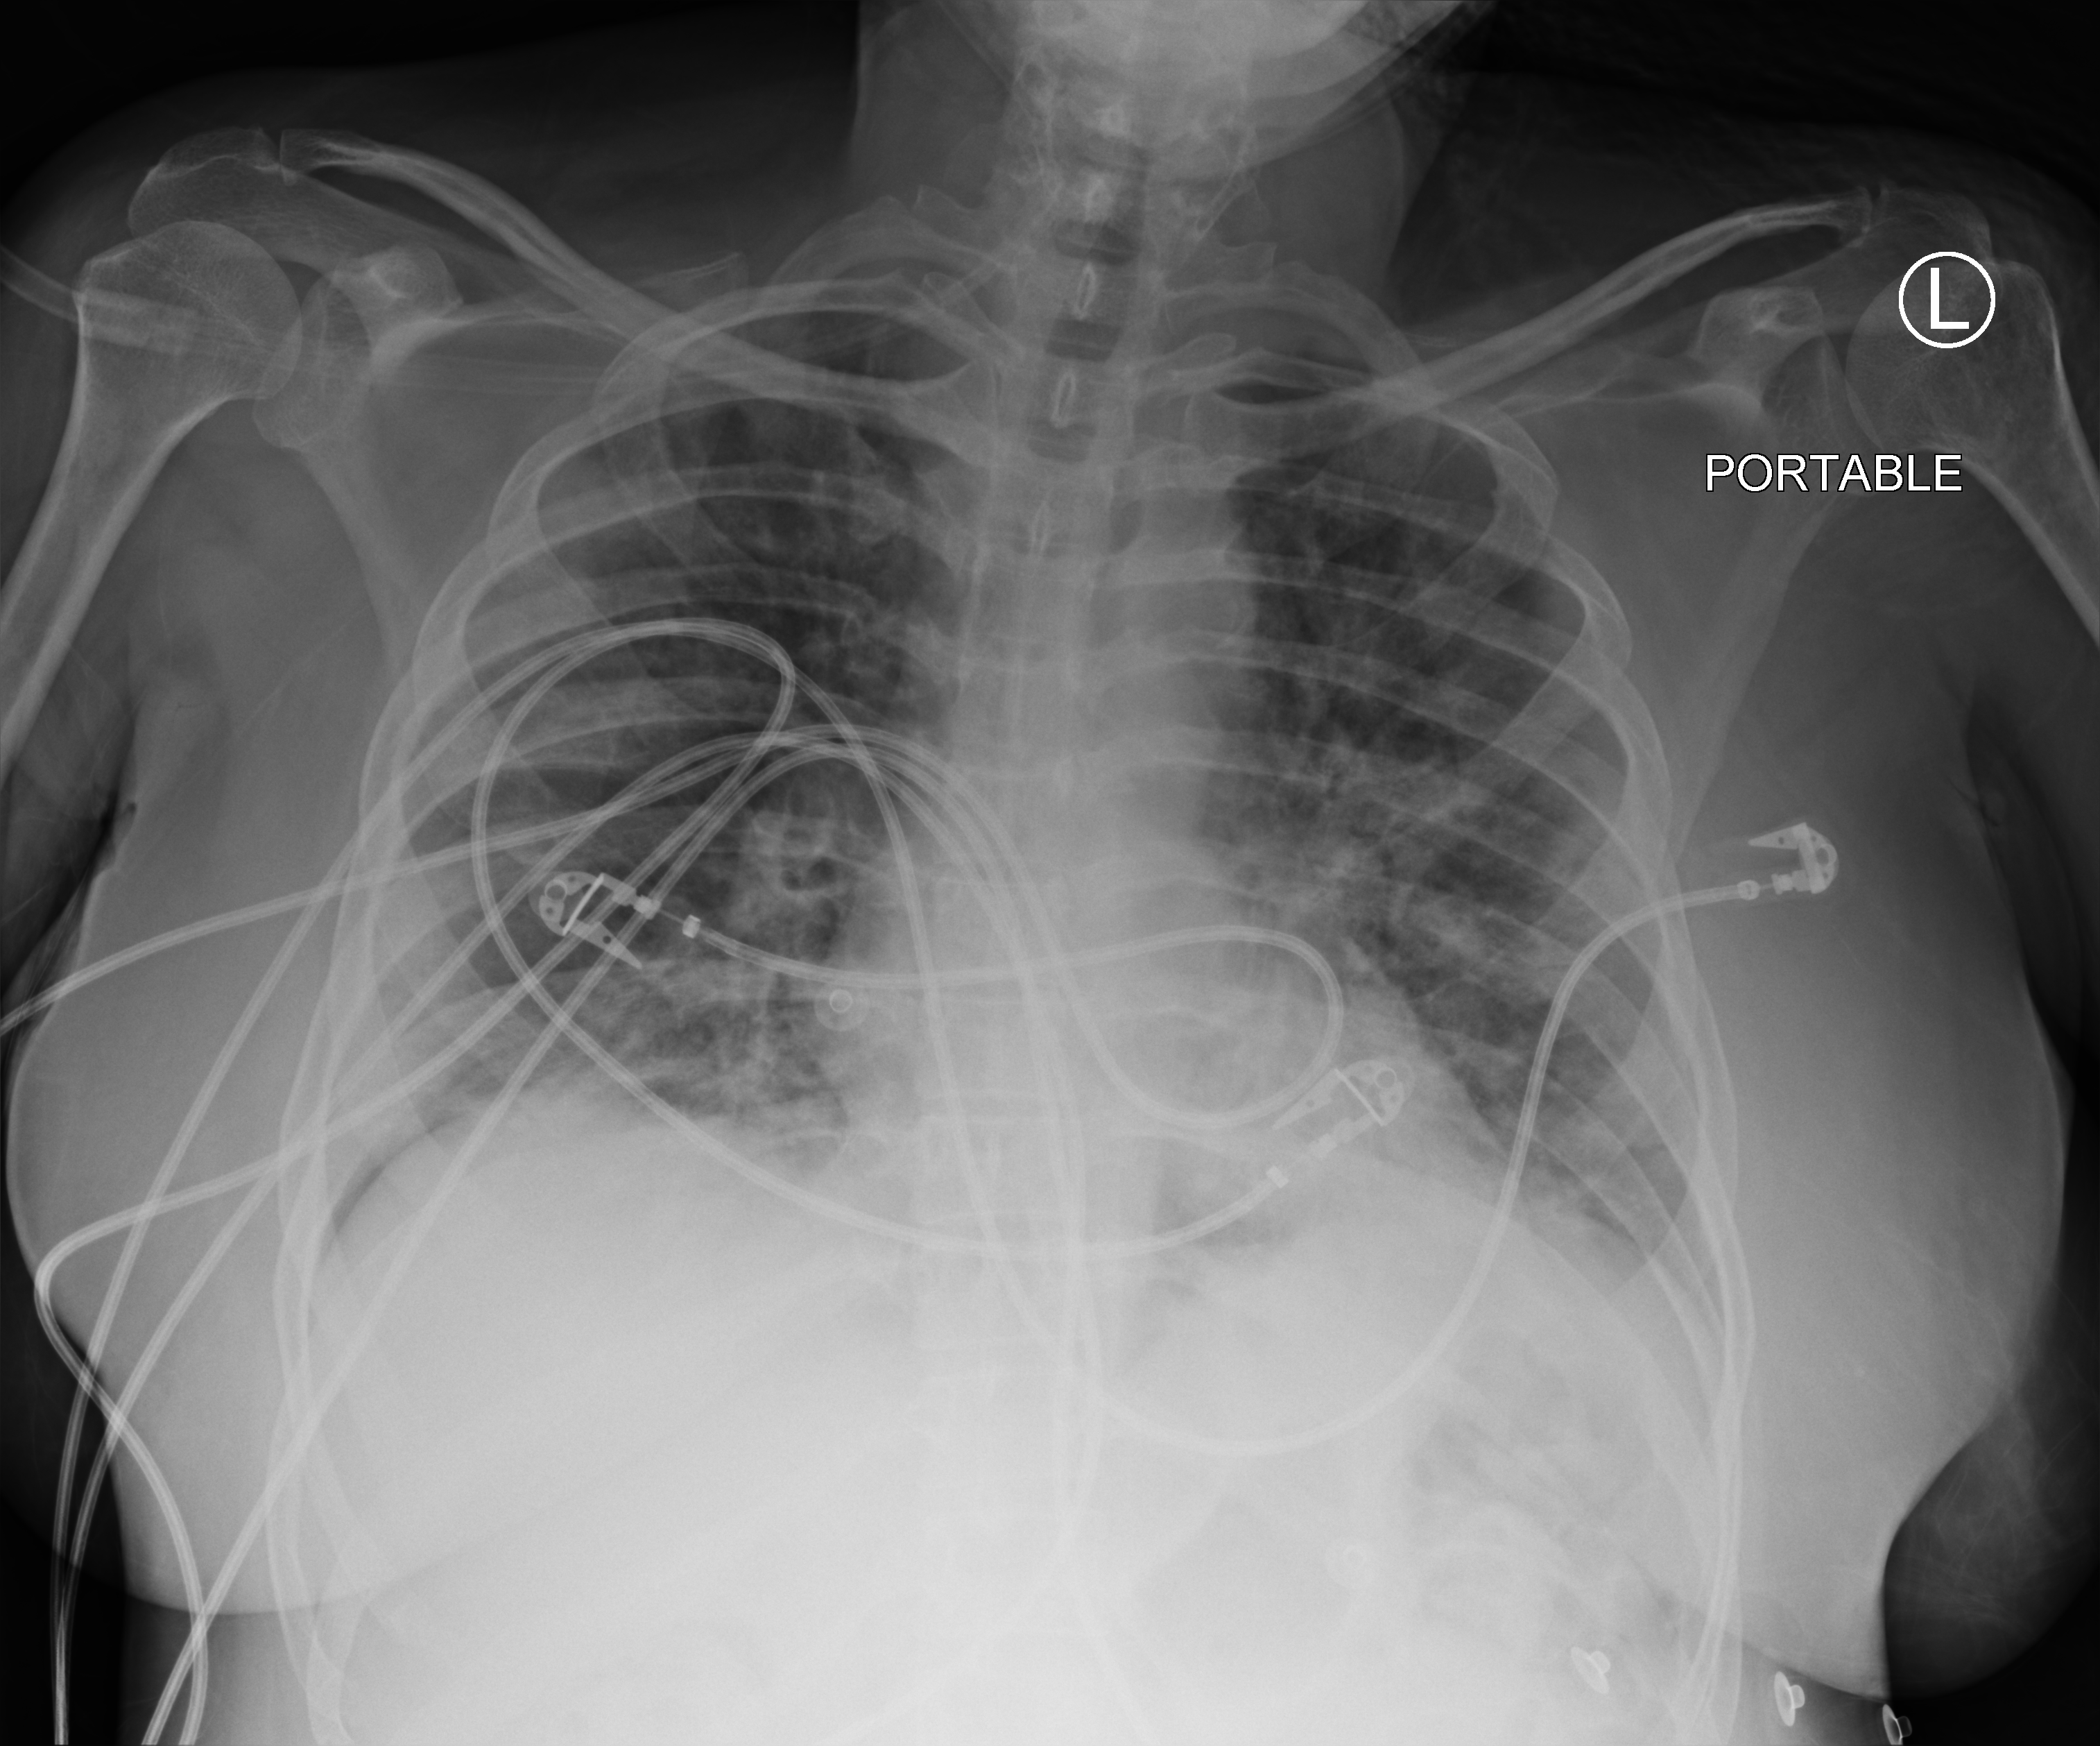
Chest X-ray (portable), anteroposterior (AP) projection. Adult patient hospitalised with COVID-19, age 18–59 years.
Hospital-stay facts (about this admission, not read from this image; timing relative to this image not recorded):
- diabetes (admission record): yes